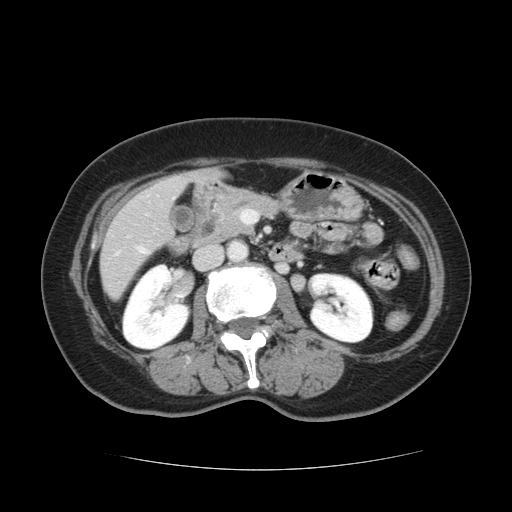
Contrast-enhanced abdominal CT, one axial slice; position 44 of 128 along the scan axis; 120 kVp; intravenous contrast given; soft-tissue window (W 400 / L 40 HU); 2.5 mm slice thickness; 512 × 512 image matrix, field of view 366 × 366 mm. Female patient, age 67 years. Case-level facts recorded for this patient, not image findings: diagnosis: colorectal cancer liver metastases, imaged before liver resection; multiple liver metastases: yes; largest metastasis: 3 cm; disease in both lobes: yes.
Annotated regions visible in this slice (manually delineated by an expert):
- hepatic veins: bounding box <140,248,145,252> (left, top, right, bottom; pixels)
- liver: <101,172,216,299>
- planned liver remnant (the part of the liver to remain after resection): <101,221,168,298>